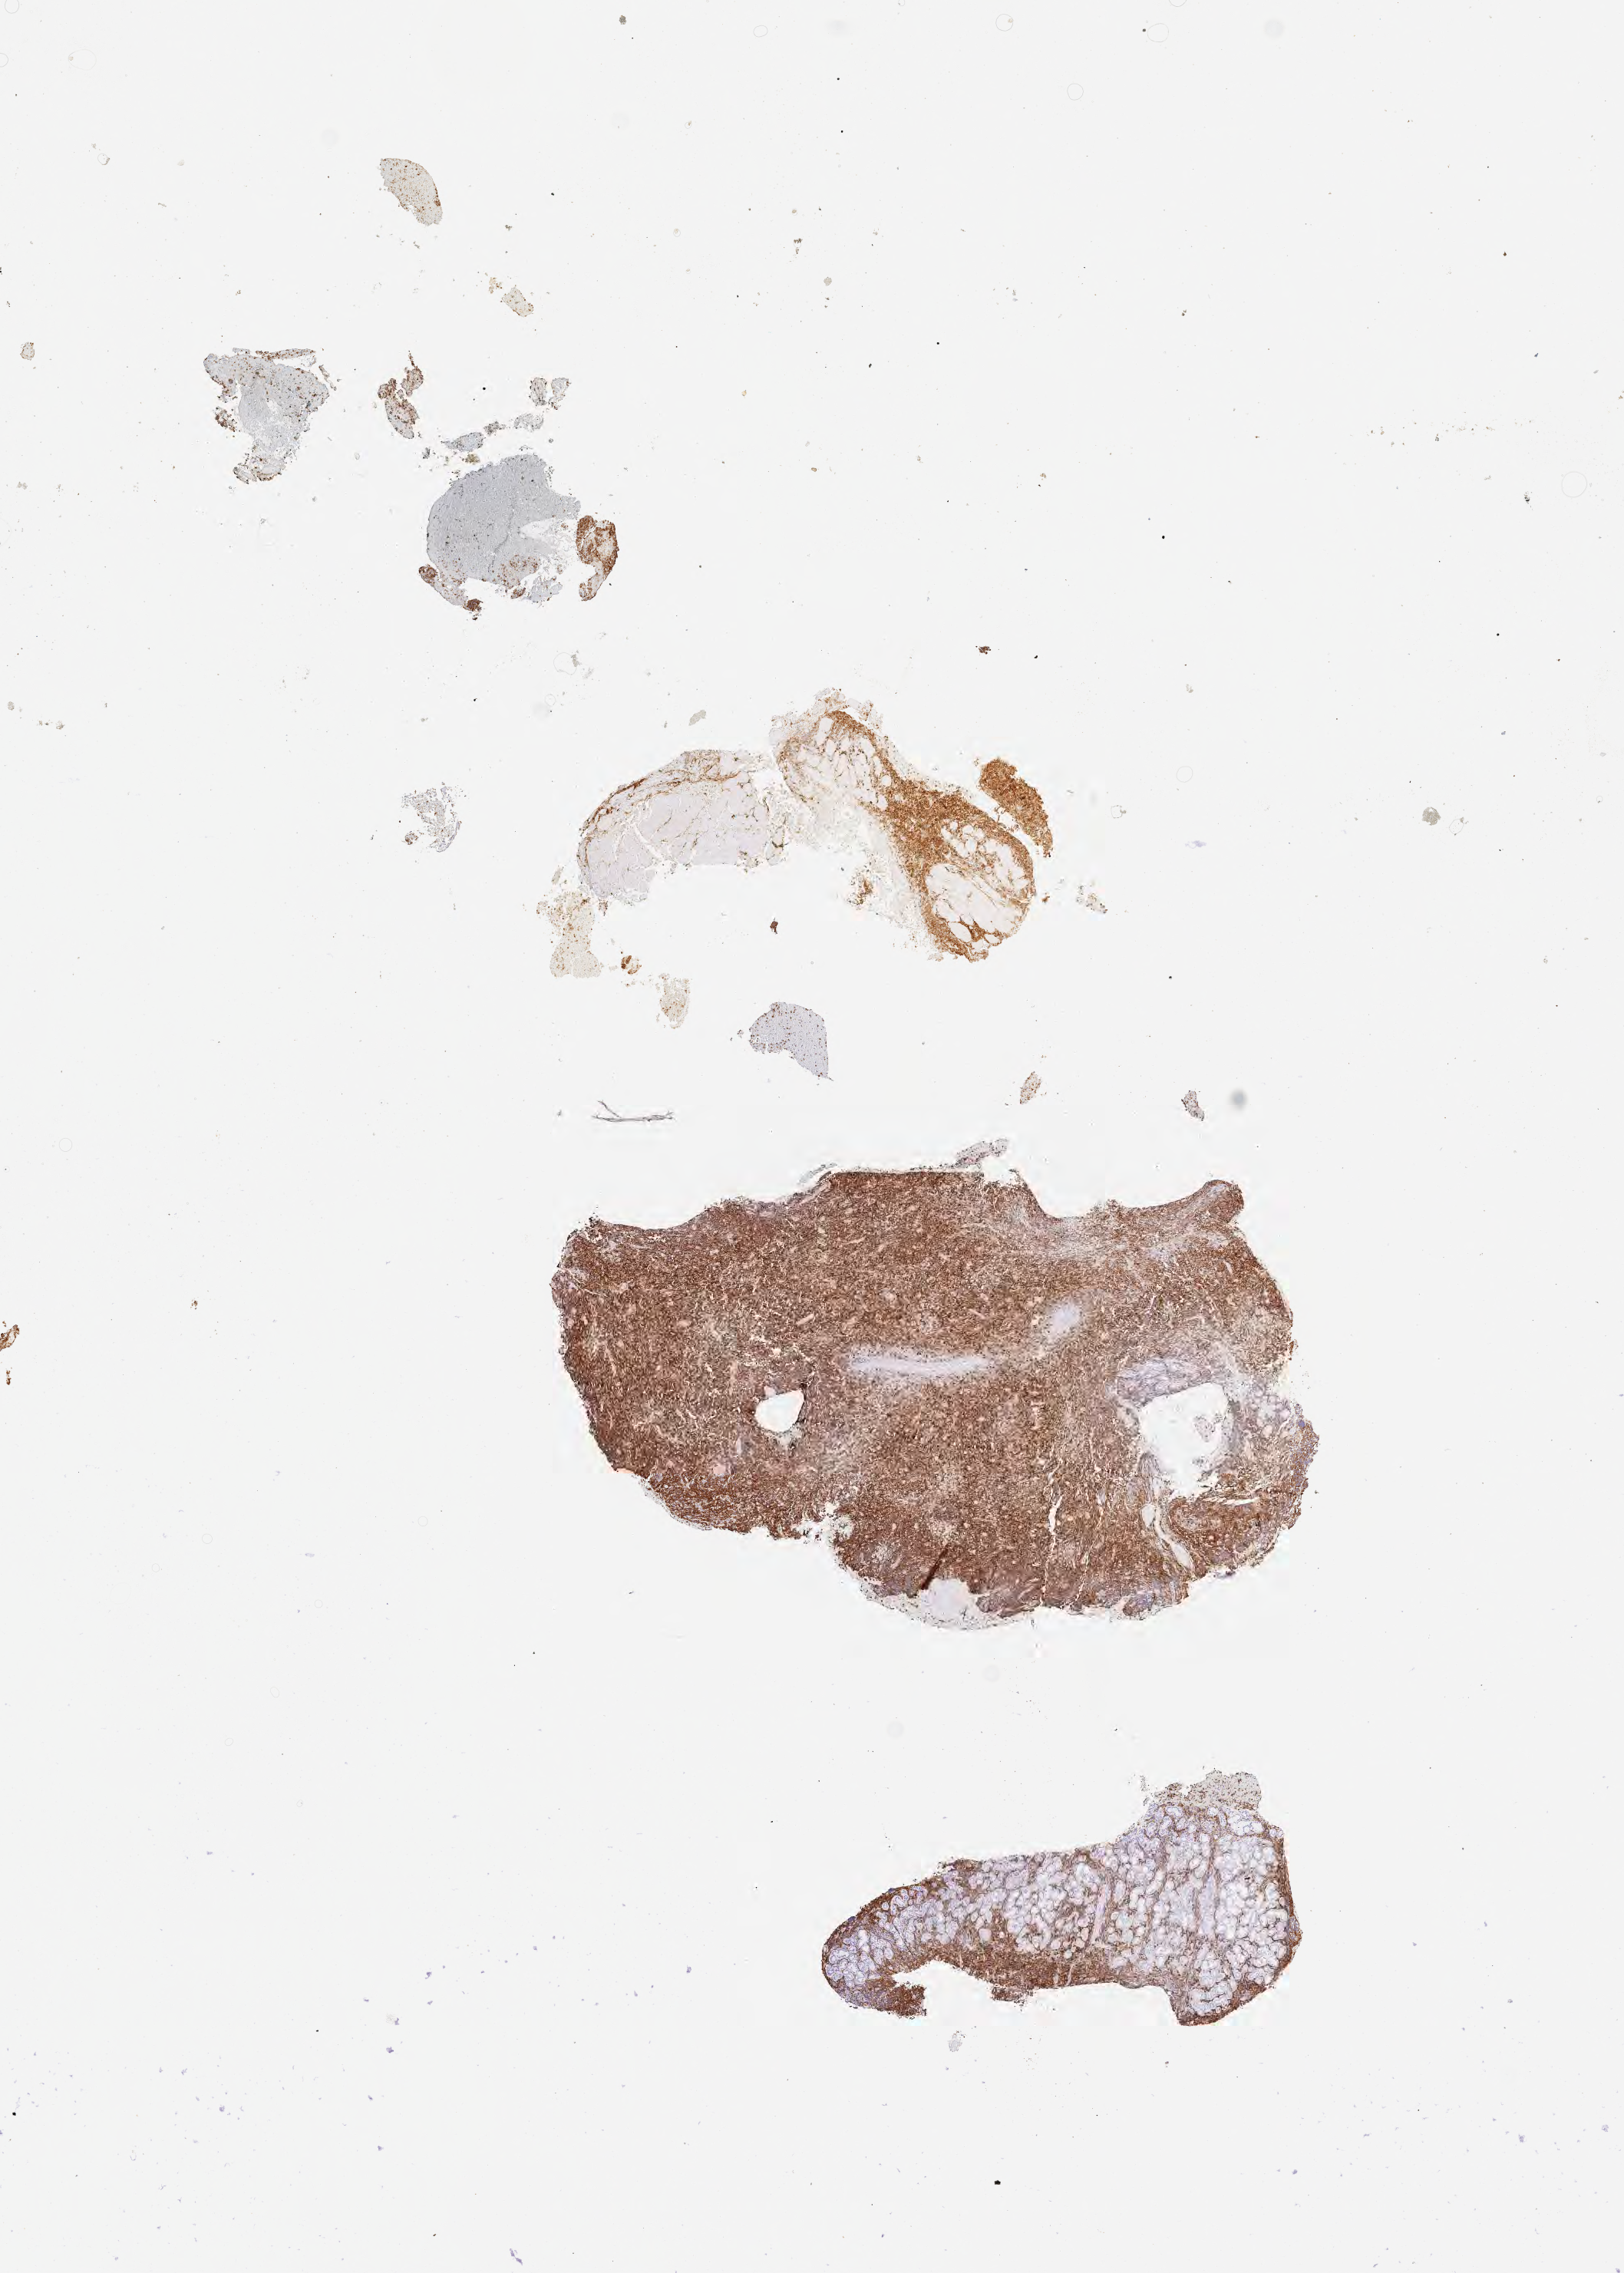
Whole-slide image, immunohistochemical stain for CD20, whole scanned area (about 8.6 x 12.0 mm) shown as a low-resolution overview. Tumor tissue. Male patient, age 53 years.
Diagnosis: Diffuse large B-cell lymphoma, NOS.